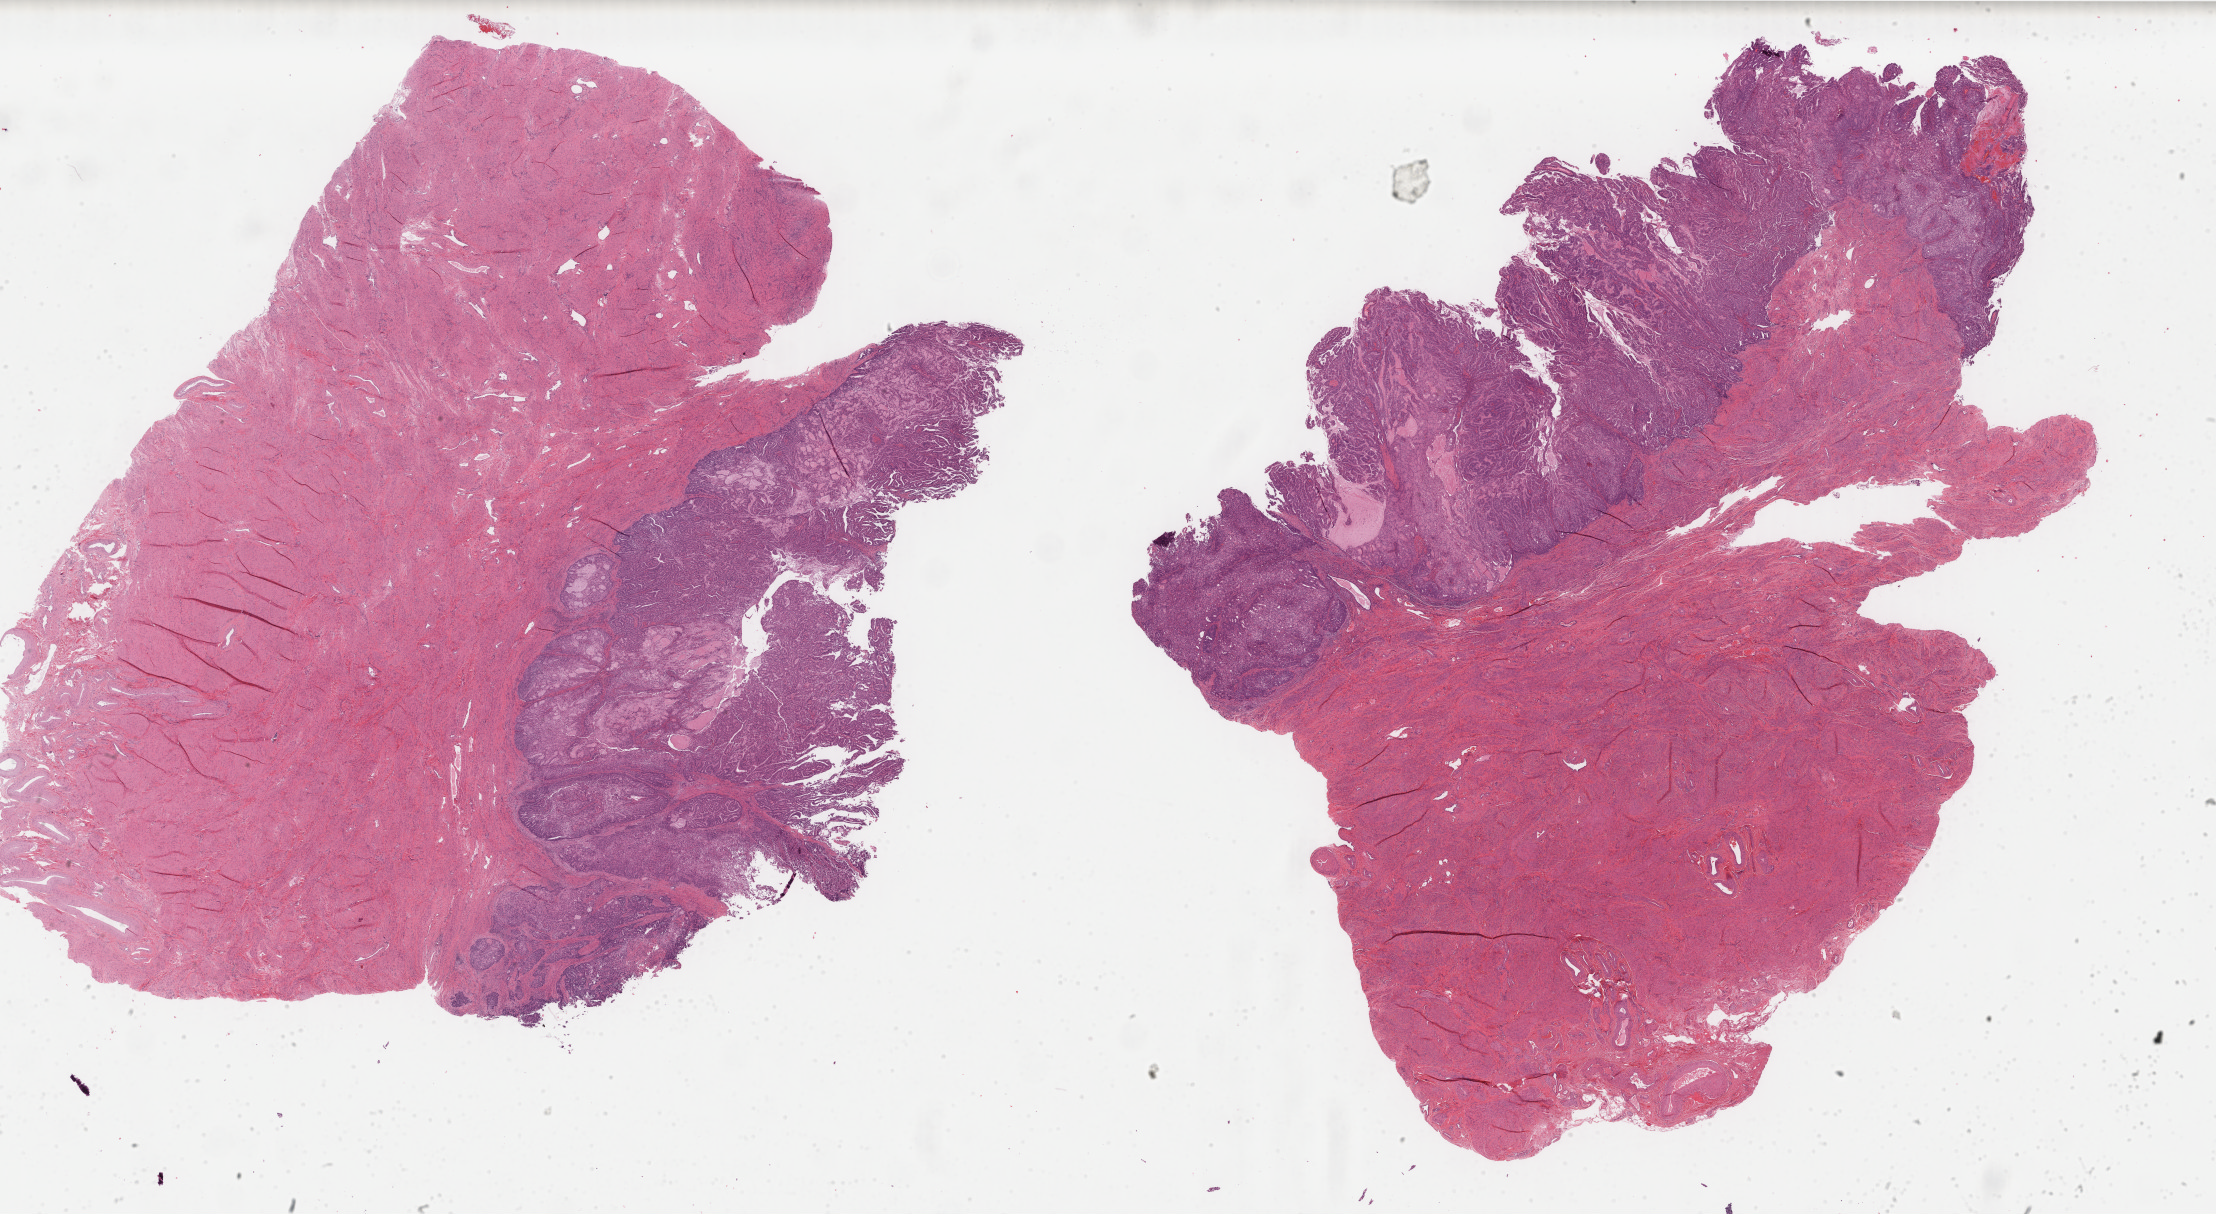
Digitized H&E-stained tissue section (whole slide) — a low-resolution overview of the entire scanned area, about 35.2 x 19.3 mm (acquisition: 40x scan). Formalin-fixed paraffin-embedded (FFPE) diagnostic section. Sample: primary tumour, uterus. Female patient; age at initial diagnosis 63 years. Histologic grade: G2 (moderately differentiated).
* FIGO stage: IV
* lymph nodes positive (case pathology): 0 of 23 examined
* diagnosis: Endometrioid adenocarcinoma, NOS (endometrium)